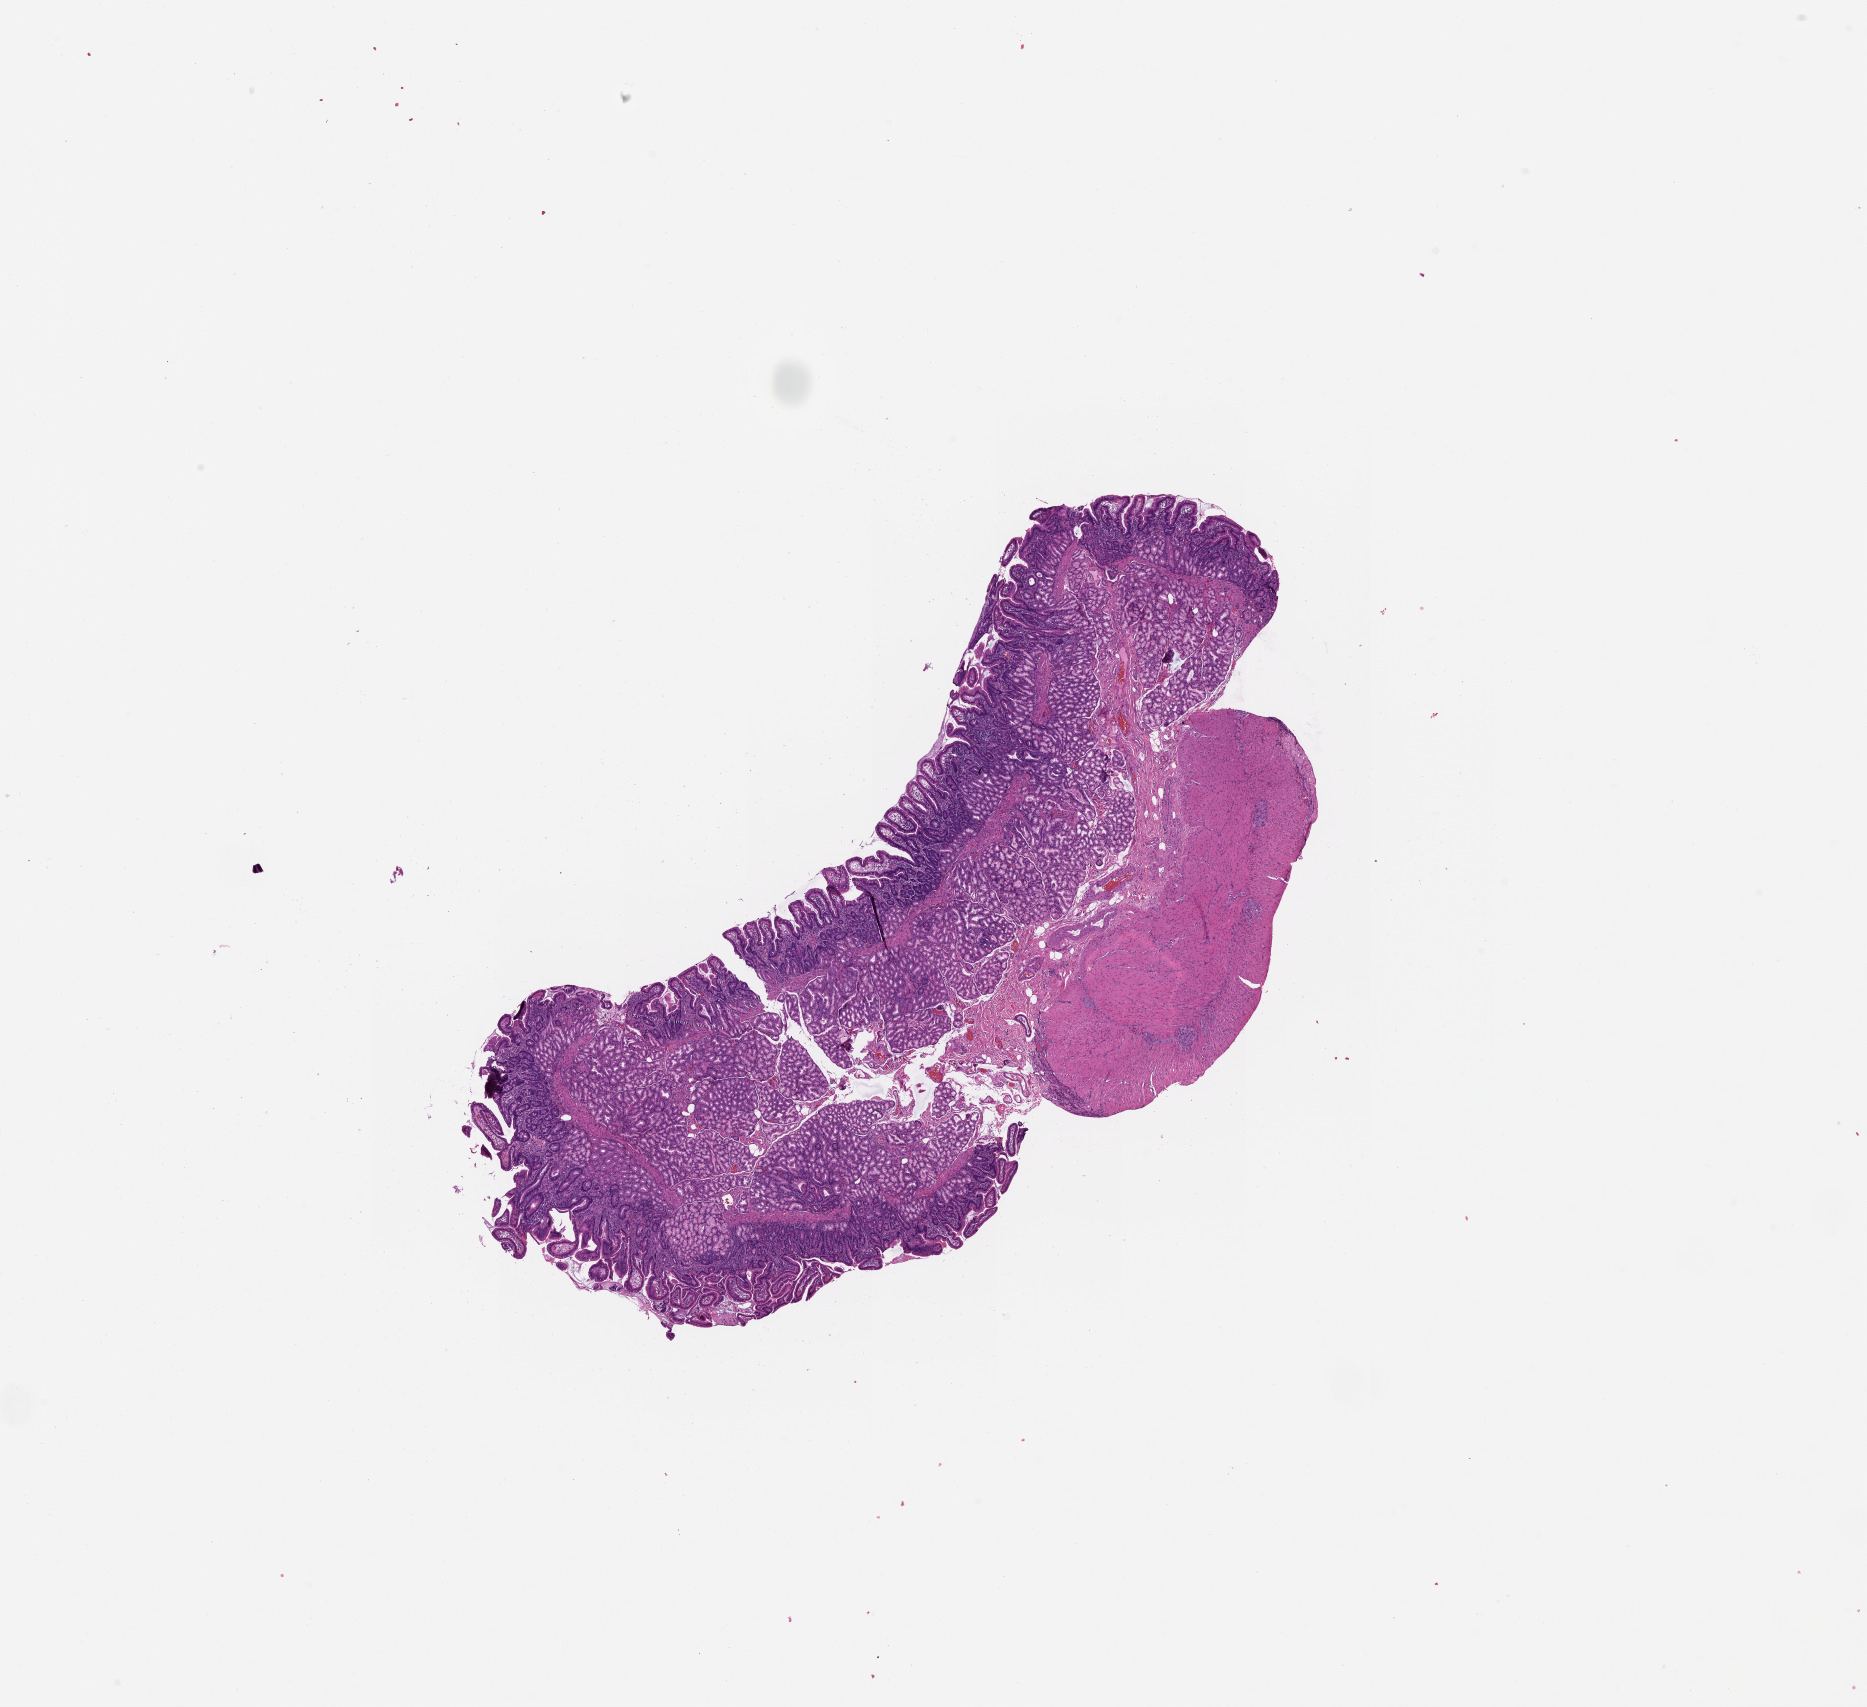
H&E whole-slide image — low-resolution overview of the scanned area, about 15.0 x 13.7 mm (from a 20x scan), pancreas, normal (non-tumour) tissue. 71-year-old female patient.
This section: normal (non-tumour) tissue from the same patient. Patient diagnosis: Infiltrating duct carcinoma, NOS.